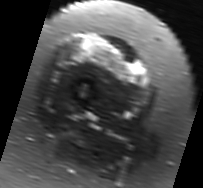
MRI of an extremity soft-tissue mass, one axial slice. Slice 20 of 91 in the series (ordered by position). T2-weighted fat-saturated. MR volume resampled by the dataset authors to the PET/CT grid (not the native acquisition matrix). 3.27 mm slice thickness. 203 × 188 image matrix. Female patient. Case-level facts recorded for this patient, not image findings: histological type: malignant solitary fibrous tumor; grade: intermediate; site of the primary tumour: right thigh.
Outlined on this slice (expert contour drawn on MRI and transferred to this co-registered scan by the dataset authors):
- gross tumour volume including surrounding oedema: bounding box (x1, y1, x2, y2) in pixels: (74, 35, 139, 82)